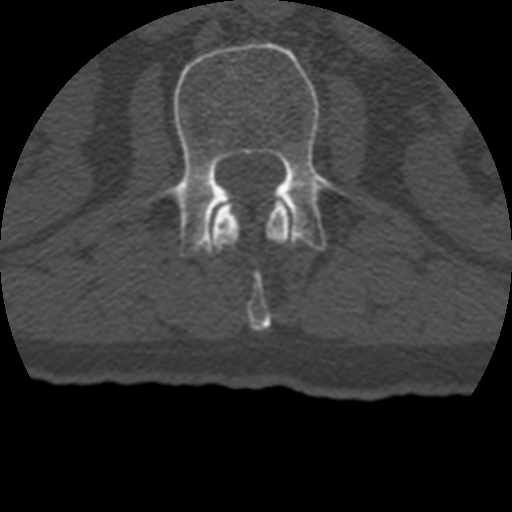
CT including the spine, one axial slice. Position 125 of 399 along the scan axis. Reconstruction kernel STANDARD. 120 kVp. Bone window (W 1800 / L 400 HU). 1.25 mm slice thickness. 512 × 512 image matrix, field of view 160 × 160 mm. Patient age 69 years. Case-level facts recorded for this patient, not image findings: primary cancer: prostate.
Structures marked on this image (semi-automatically segmented with operator editing):
- L1 vertebra: bounding box [x1, y1, x2, y2] px = [211, 198, 293, 331]
- L2 vertebra: [124, 42, 341, 256]